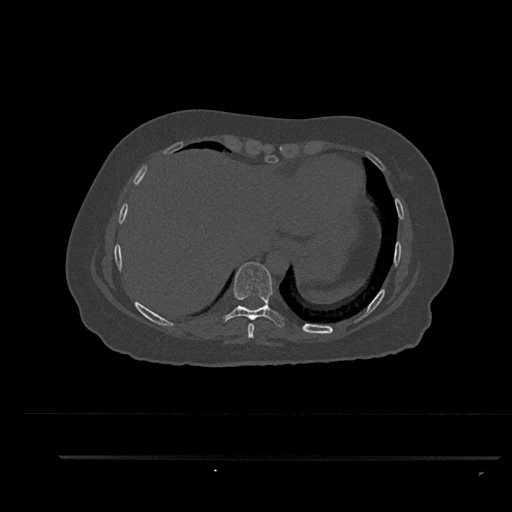
CT including the spine, one axial slice; slice 417 of 797 in the series (ordered by position); reconstruction kernel Br40s/3; 120 kVp; bone window (W 1800 / L 400 HU); 512 × 512 image matrix, field of view 408 × 408 mm. Female patient, age 44 years. Case-level facts recorded for this patient, not image findings: primary cancer: renal.
Structures marked on this image (semi-automatic segmentation, software-assisted and operator-edited):
- T8 vertebra: bounding box [x1, y1, x2, y2] px = [247, 323, 255, 338]
- T9 vertebra: [221, 262, 285, 328]